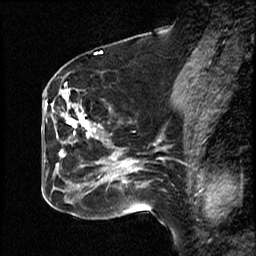
Breast MRI (dynamic contrast-enhanced), one sagittal slice. Position 26 of 50 along the scan axis. Dynamic contrast-enhanced study with each time point stored as its own series, time point 2 of 4 at this slice position (early post-contrast, ordered by acquisition time). 1.5 T. TE 4.2 ms, TR 18.5 ms. 3 mm slice thickness. 256 × 256 image matrix, field of view 200 × 200 mm. Female patient, age 44 years. Case-level facts recorded for this patient, not image findings: setting: breast cancer imaged before/during neoadjuvant chemotherapy; receptor status: HR-positive, HER2-negative.
Annotated regions visible in this slice (semi-automatic segmentation, software-assisted and operator-edited):
- analysis volume of interest (the breast-tissue region the enhancement analysis was run in; not a lesion): box from (x=59, y=84) to (x=114, y=205) px
- tumour enhancement mask (voxels above the 100 % enhancement threshold inside the analysis volume of interest): (x=59, y=90)–(x=114, y=180)